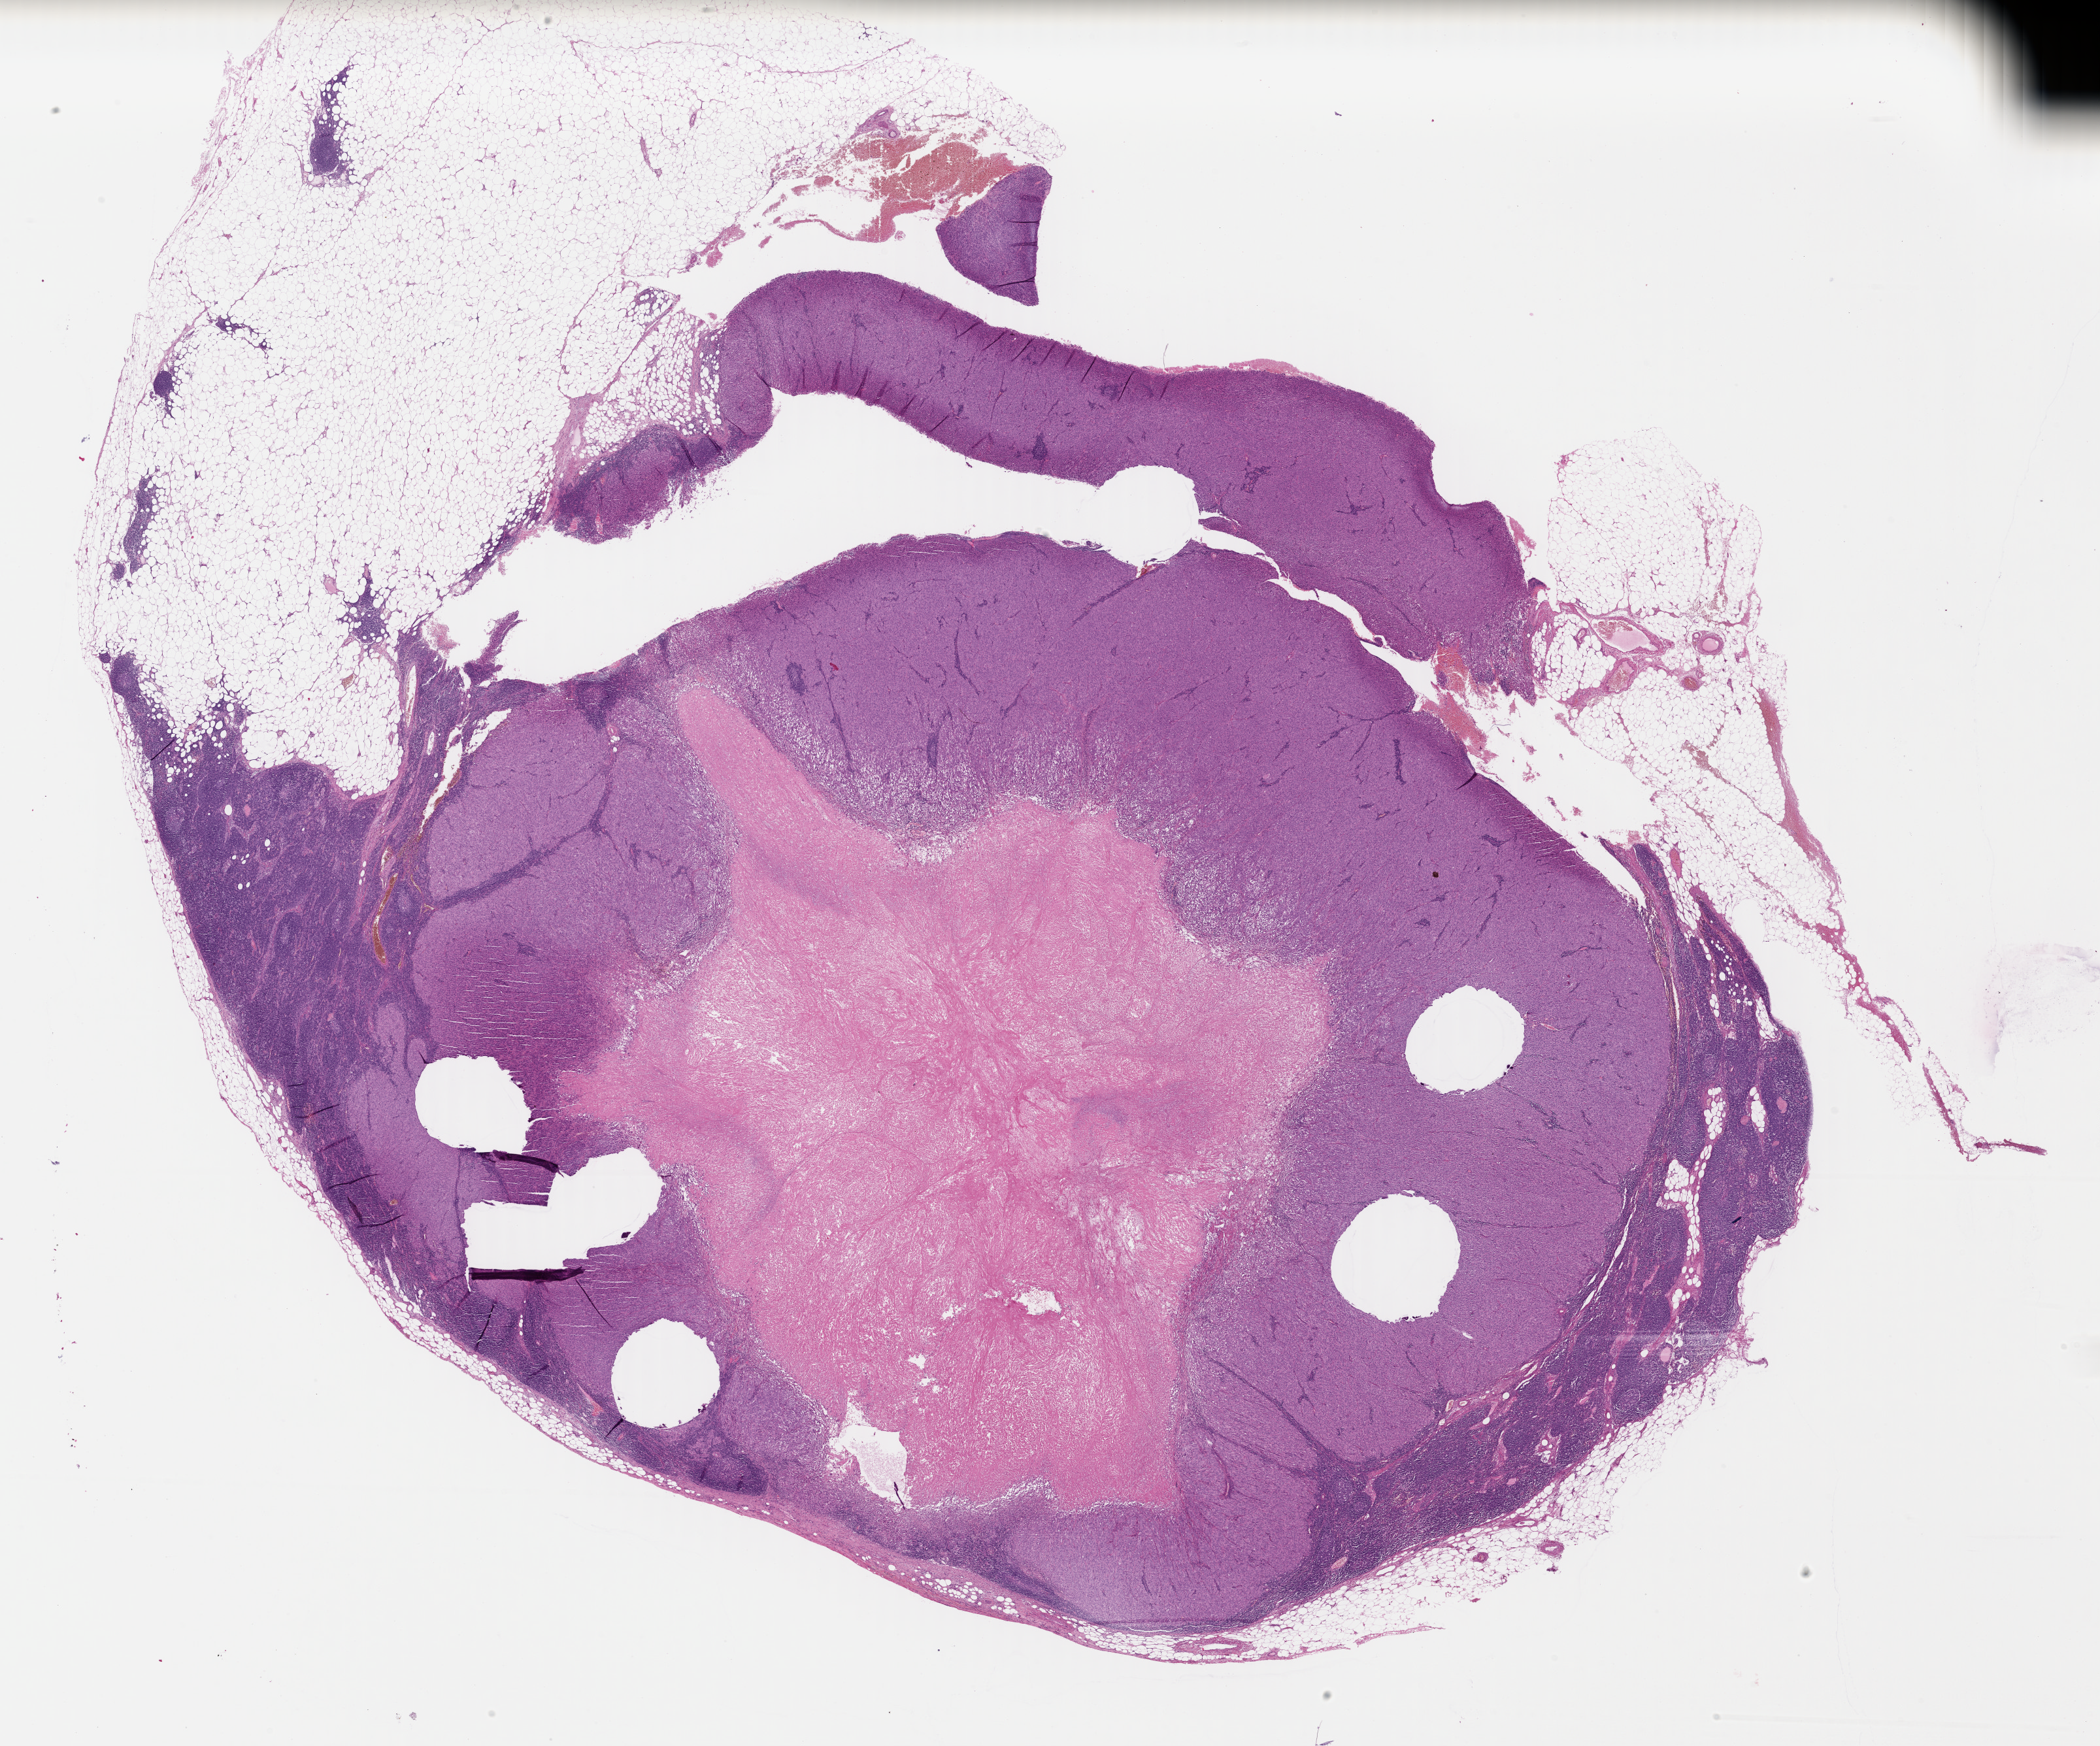
Digitized H&E tissue section (whole slide), a low-resolution overview of the entire scanned area, about 25.3 x 21.0 mm, formalin-fixed paraffin-embedded (FFPE) diagnostic section, primary tumour sample from the skin. Male, age 60 years at initial diagnosis.
Histologic diagnosis: Malignant melanoma, NOS.